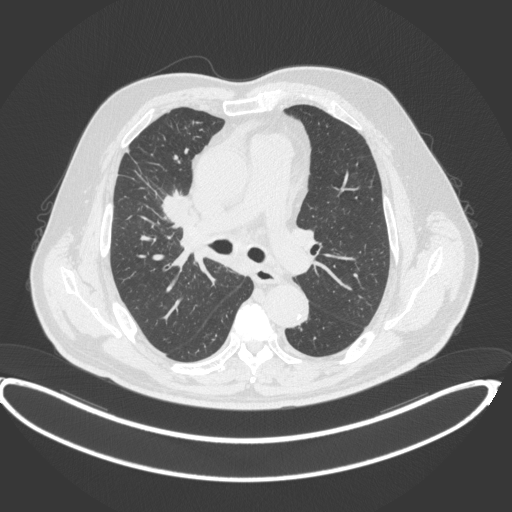
Chest CT, one axial slice; 120 kVp; lung window (W 1500 / L -600 HU); 1 mm slice thickness; 512 × 512 image matrix, field of view 448 × 448 mm. Patient: male, 62 years. Case-level facts recorded for this patient, not image findings: clinical TNM (as recorded): T1c N3 M1c.
Annotated regions visible in this slice (rectangle marked by the reading radiologist):
- lung tumour (recorded histology: adenocarcinoma): bounding box (x1, y1, x2, y2) in pixels: (160, 189, 192, 226)